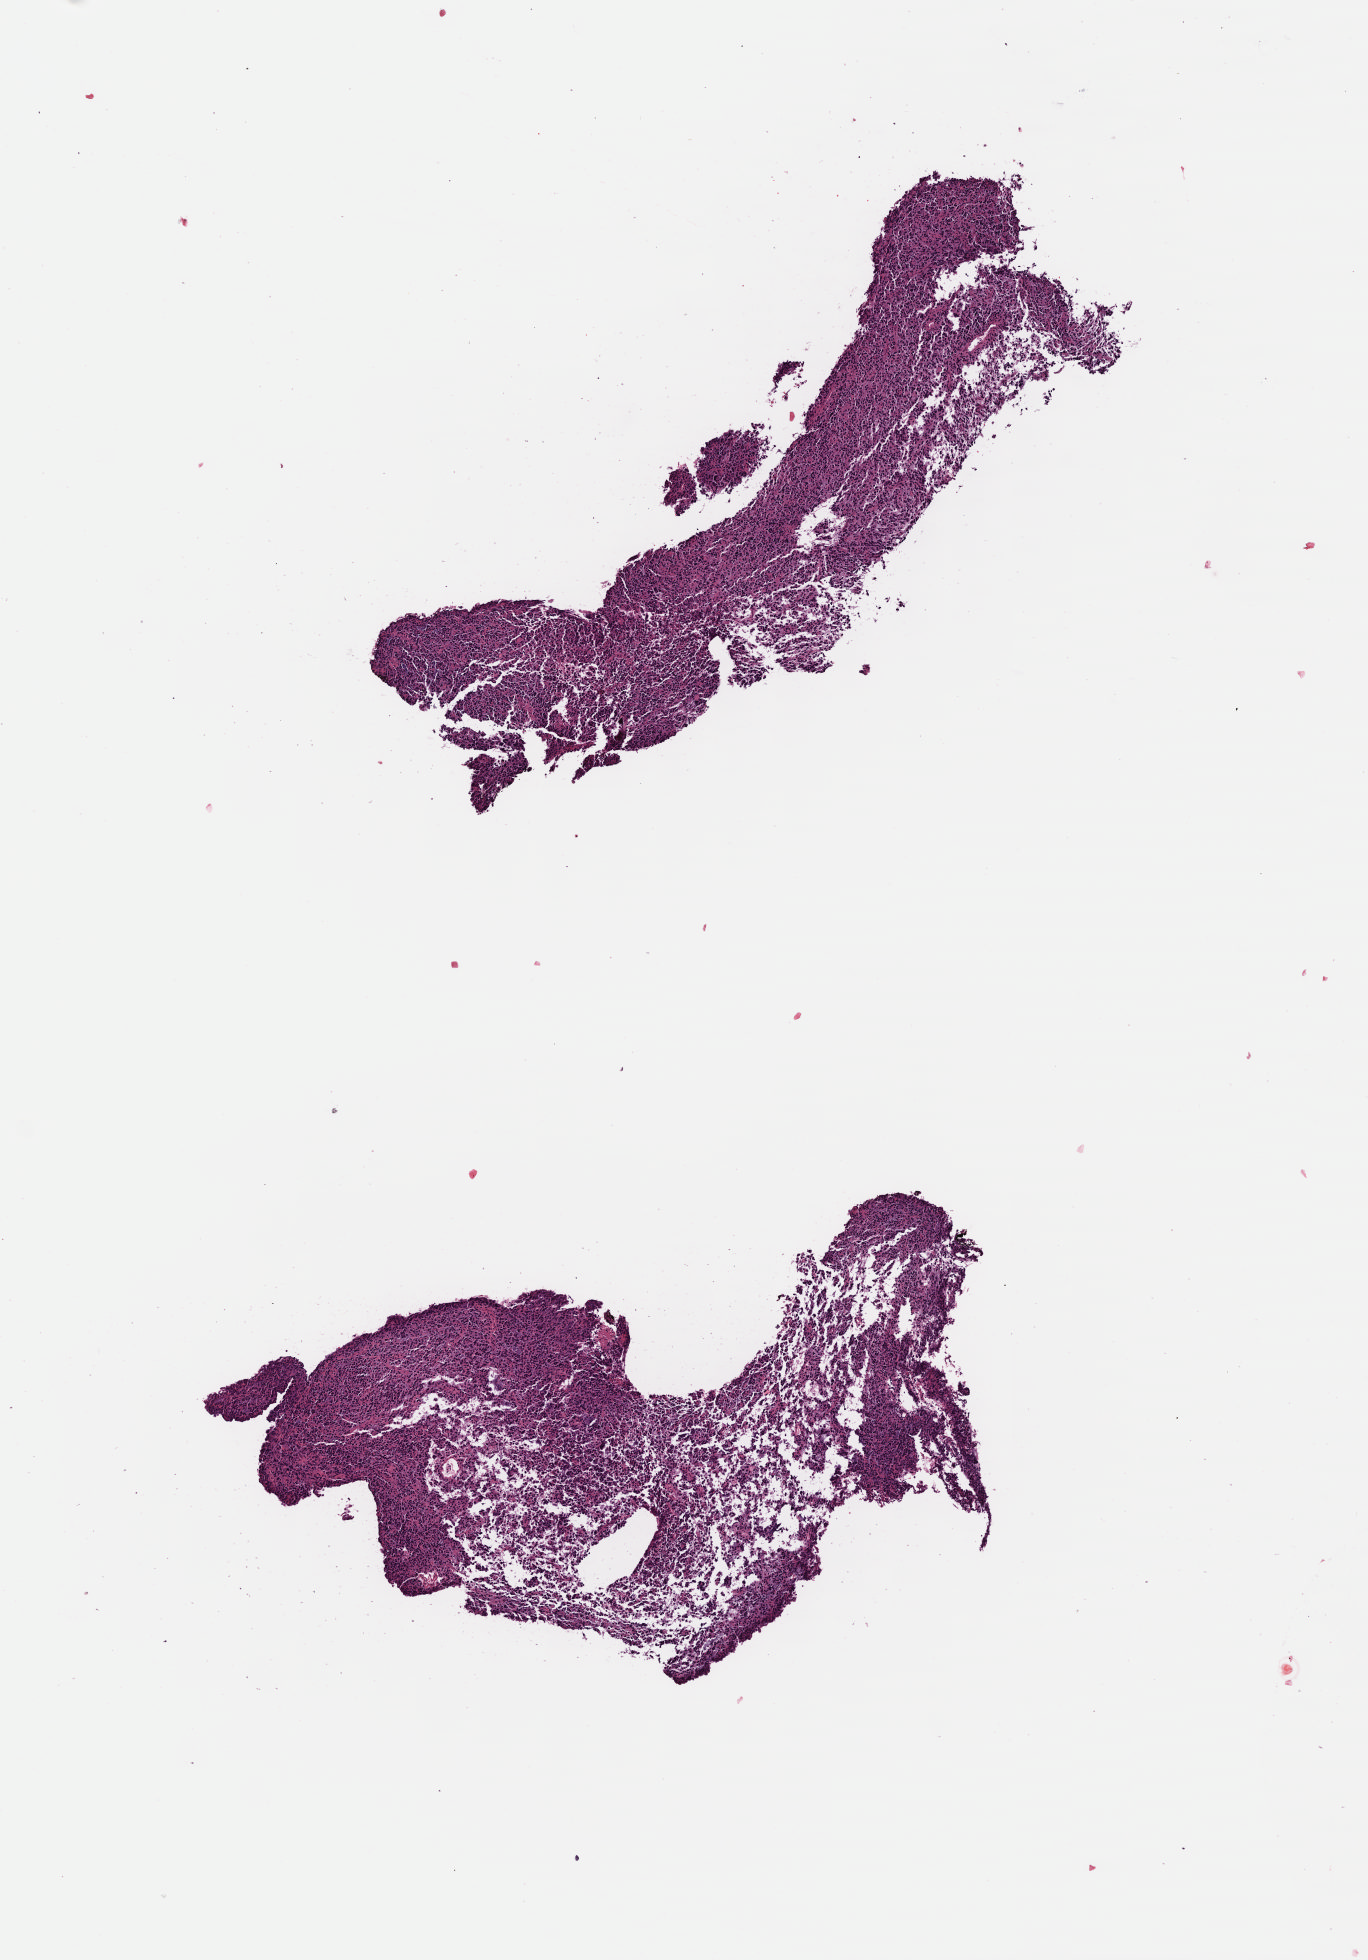
H&E whole-slide image — shown as a low-resolution overview of the whole scanned area (about 5.4 x 7.7 mm). Formalin-fixed paraffin-embedded (FFPE) diagnostic section. Primary tumour sample from the brain. Patient: male, age at initial diagnosis 29 years. Histologic grade: G2 (moderately differentiated).
Histologic diagnosis: Mixed glioma (cerebrum).